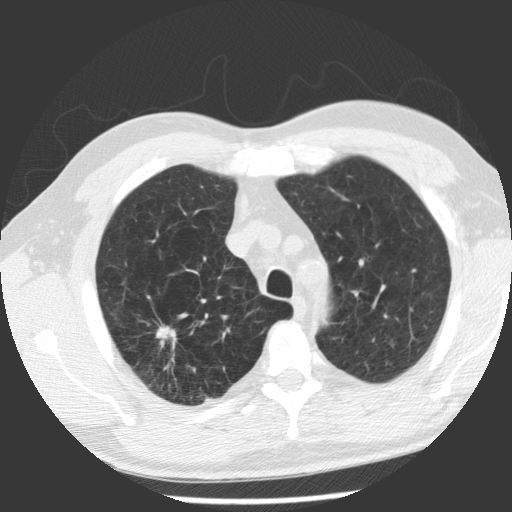
Low-dose screening chest CT, one axial slice. Position 88 of 112 along the scan axis. Reconstruction kernel STANDARD. 140 kVp. Lung window (W 1500 / L -600 HU). 512 × 512 image matrix, field of view 344 × 344 mm.
Annotated regions visible in this slice (manually delineated by an expert):
- lesion 1 (tumor, upper lobe of right lung): bounding box [x1, y1, x2, y2] px = [156, 325, 169, 346]